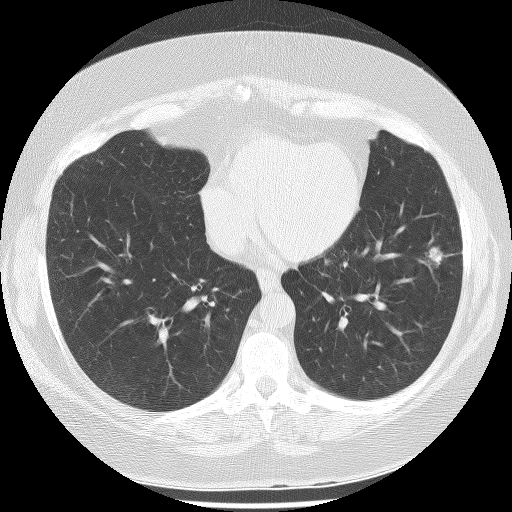
Low-dose screening chest CT, axial slice; first (baseline) screen; lung window (W 1500 / L -600 HU); lung (sharp) reconstruction kernel (BONE); 120 kVp. Female, age 56 years at enrolment. Former smoker at enrolment.
• Expert-annotated lung lesion, bounding box [x1, y1, x2, y2] px = [390, 224, 465, 286].
• Reader record for this screening exam (exam-level; its link to the box is not recorded): non-calcified nodule or mass ≥4 mm, left lower lobe, 22 × 17 mm, spiculated (stellate) margins, soft tissue attenuation.
• Later outcome: lung cancer diagnosed 63 days after this screen — bronchiolo-alveolar adenocarcinoma, NOS, left lower lobe, stage IA (AJCC 6th edition), 18 mm at pathology.